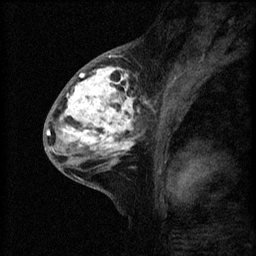
Breast MRI (dynamic contrast-enhanced), one sagittal slice; position 29 of 60 along the scan axis; 3 images stored at this slice position (order not interpretable as contrast timing); 1.5 T; TE 4.2 ms, TR 8.2 ms; 2 mm slice thickness; 256 × 256 image matrix, field of view 180 × 180 mm. Female patient, age 41 years.
Structures marked on this image (semi-automatic segmentation, software-assisted and operator-edited):
- analysis volume of interest (the breast-tissue region the enhancement analysis was run in; not a lesion): box from (x=53, y=62) to (x=160, y=175) px
- tumour enhancement mask (voxels above the 70 % enhancement threshold inside the analysis volume of interest): (x=53, y=66)–(x=149, y=157)